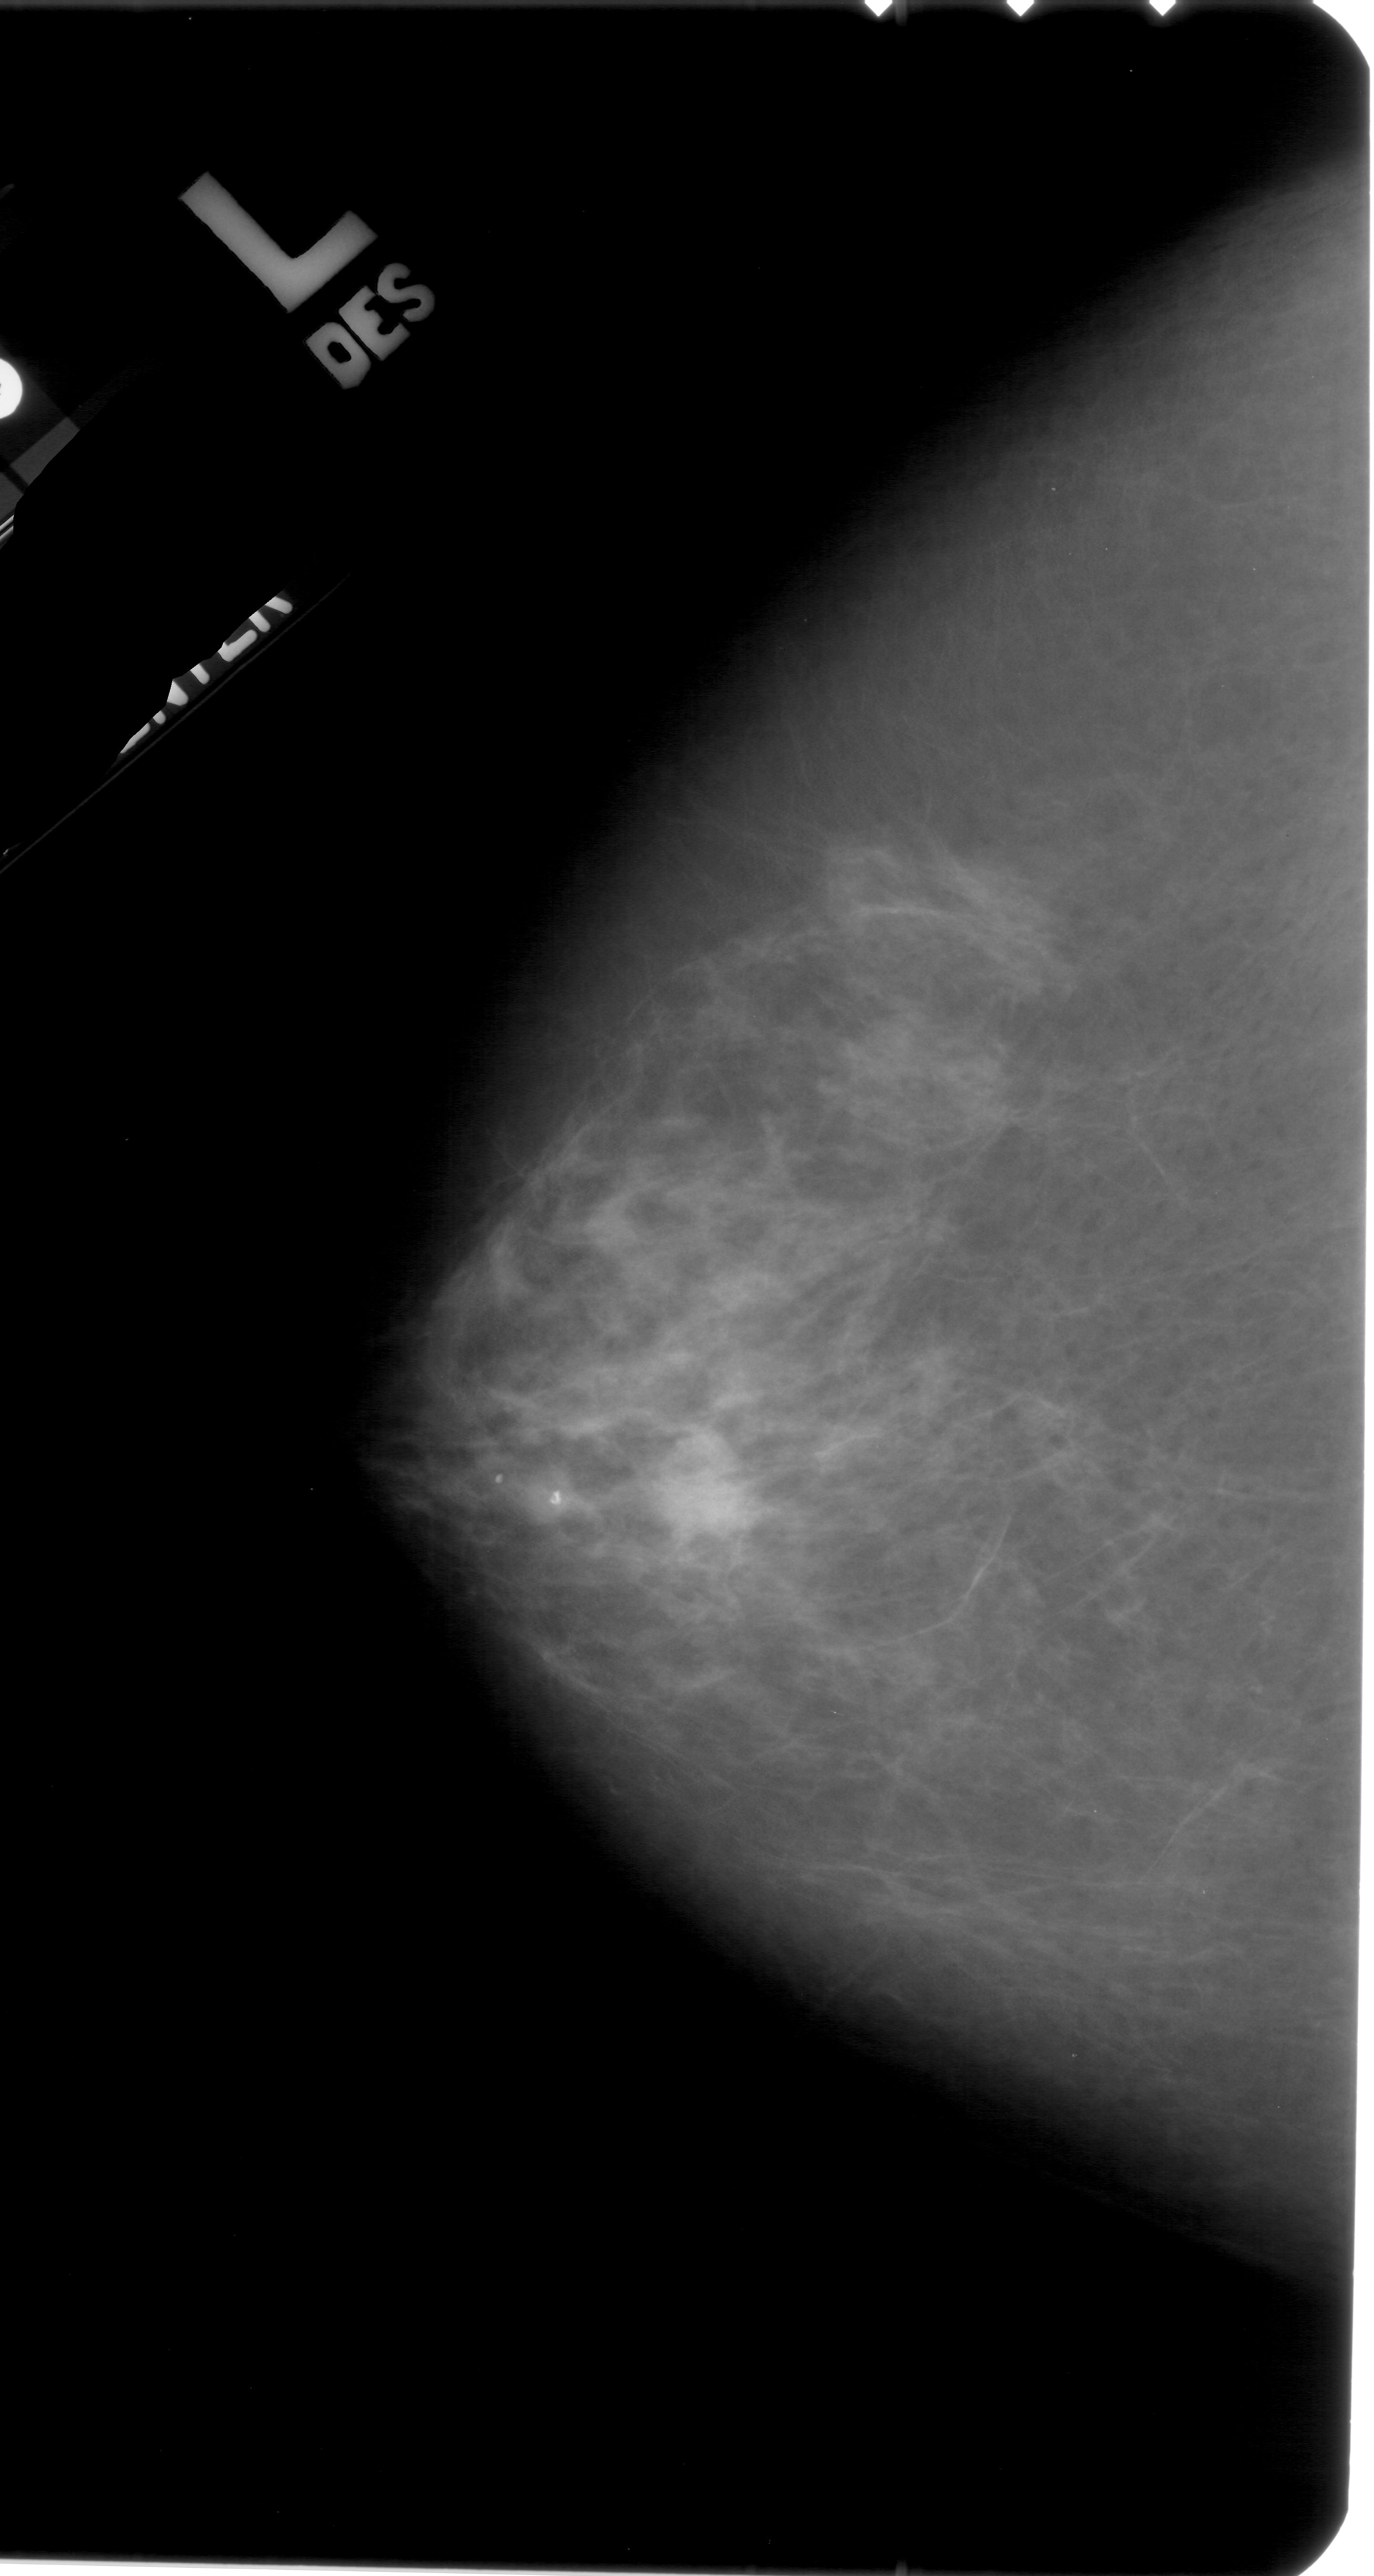
Digitized screen-film mammogram; left breast; CC view; BI-RADS breast density category 2 (scale 1–4).
- Marked abnormality: mass, shape irregular, margins ill defined; BI-RADS assessment category 4; pathology (as recorded): malignant.